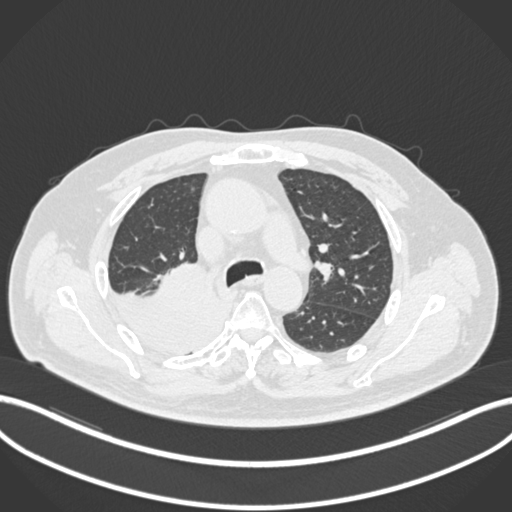
Chest CT, one axial slice. Position 135 of 218 along the scan axis. Reconstruction kernel B30f. 120 kVp. Lung window (W 1500 / L -600 HU). 512 × 512 image matrix, field of view 400 × 400 mm. Patient: male, 68 years. From the clinical record (not read from this slice): clinical TNM (as recorded): T2a N0 M0.
Structures marked on this image (rectangle marked by the reading radiologist):
- lung tumour (recorded histology: adenocarcinoma): bounding box <109,265,235,360> (left, top, right, bottom; pixels)